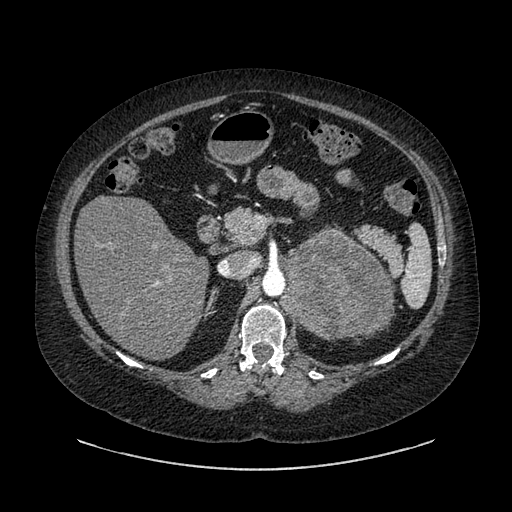
Contrast-enhanced abdominal CT, one axial slice. Position 562 of 769 along the scan axis. Intravenous contrast given. Soft-tissue window (W 400 / L 40 HU). 512 × 512 image matrix, field of view 460 × 460 mm. Female patient, age 61 years. From the clinical record (not read from this slice): diagnosis: adrenocortical carcinoma; tumour side: left adrenal; tumour size at pathology: 13 cm.
Structures marked on this image (semi-automatically segmented with operator editing):
- mass: bounding box <282,230,391,340> (left, top, right, bottom; pixels)